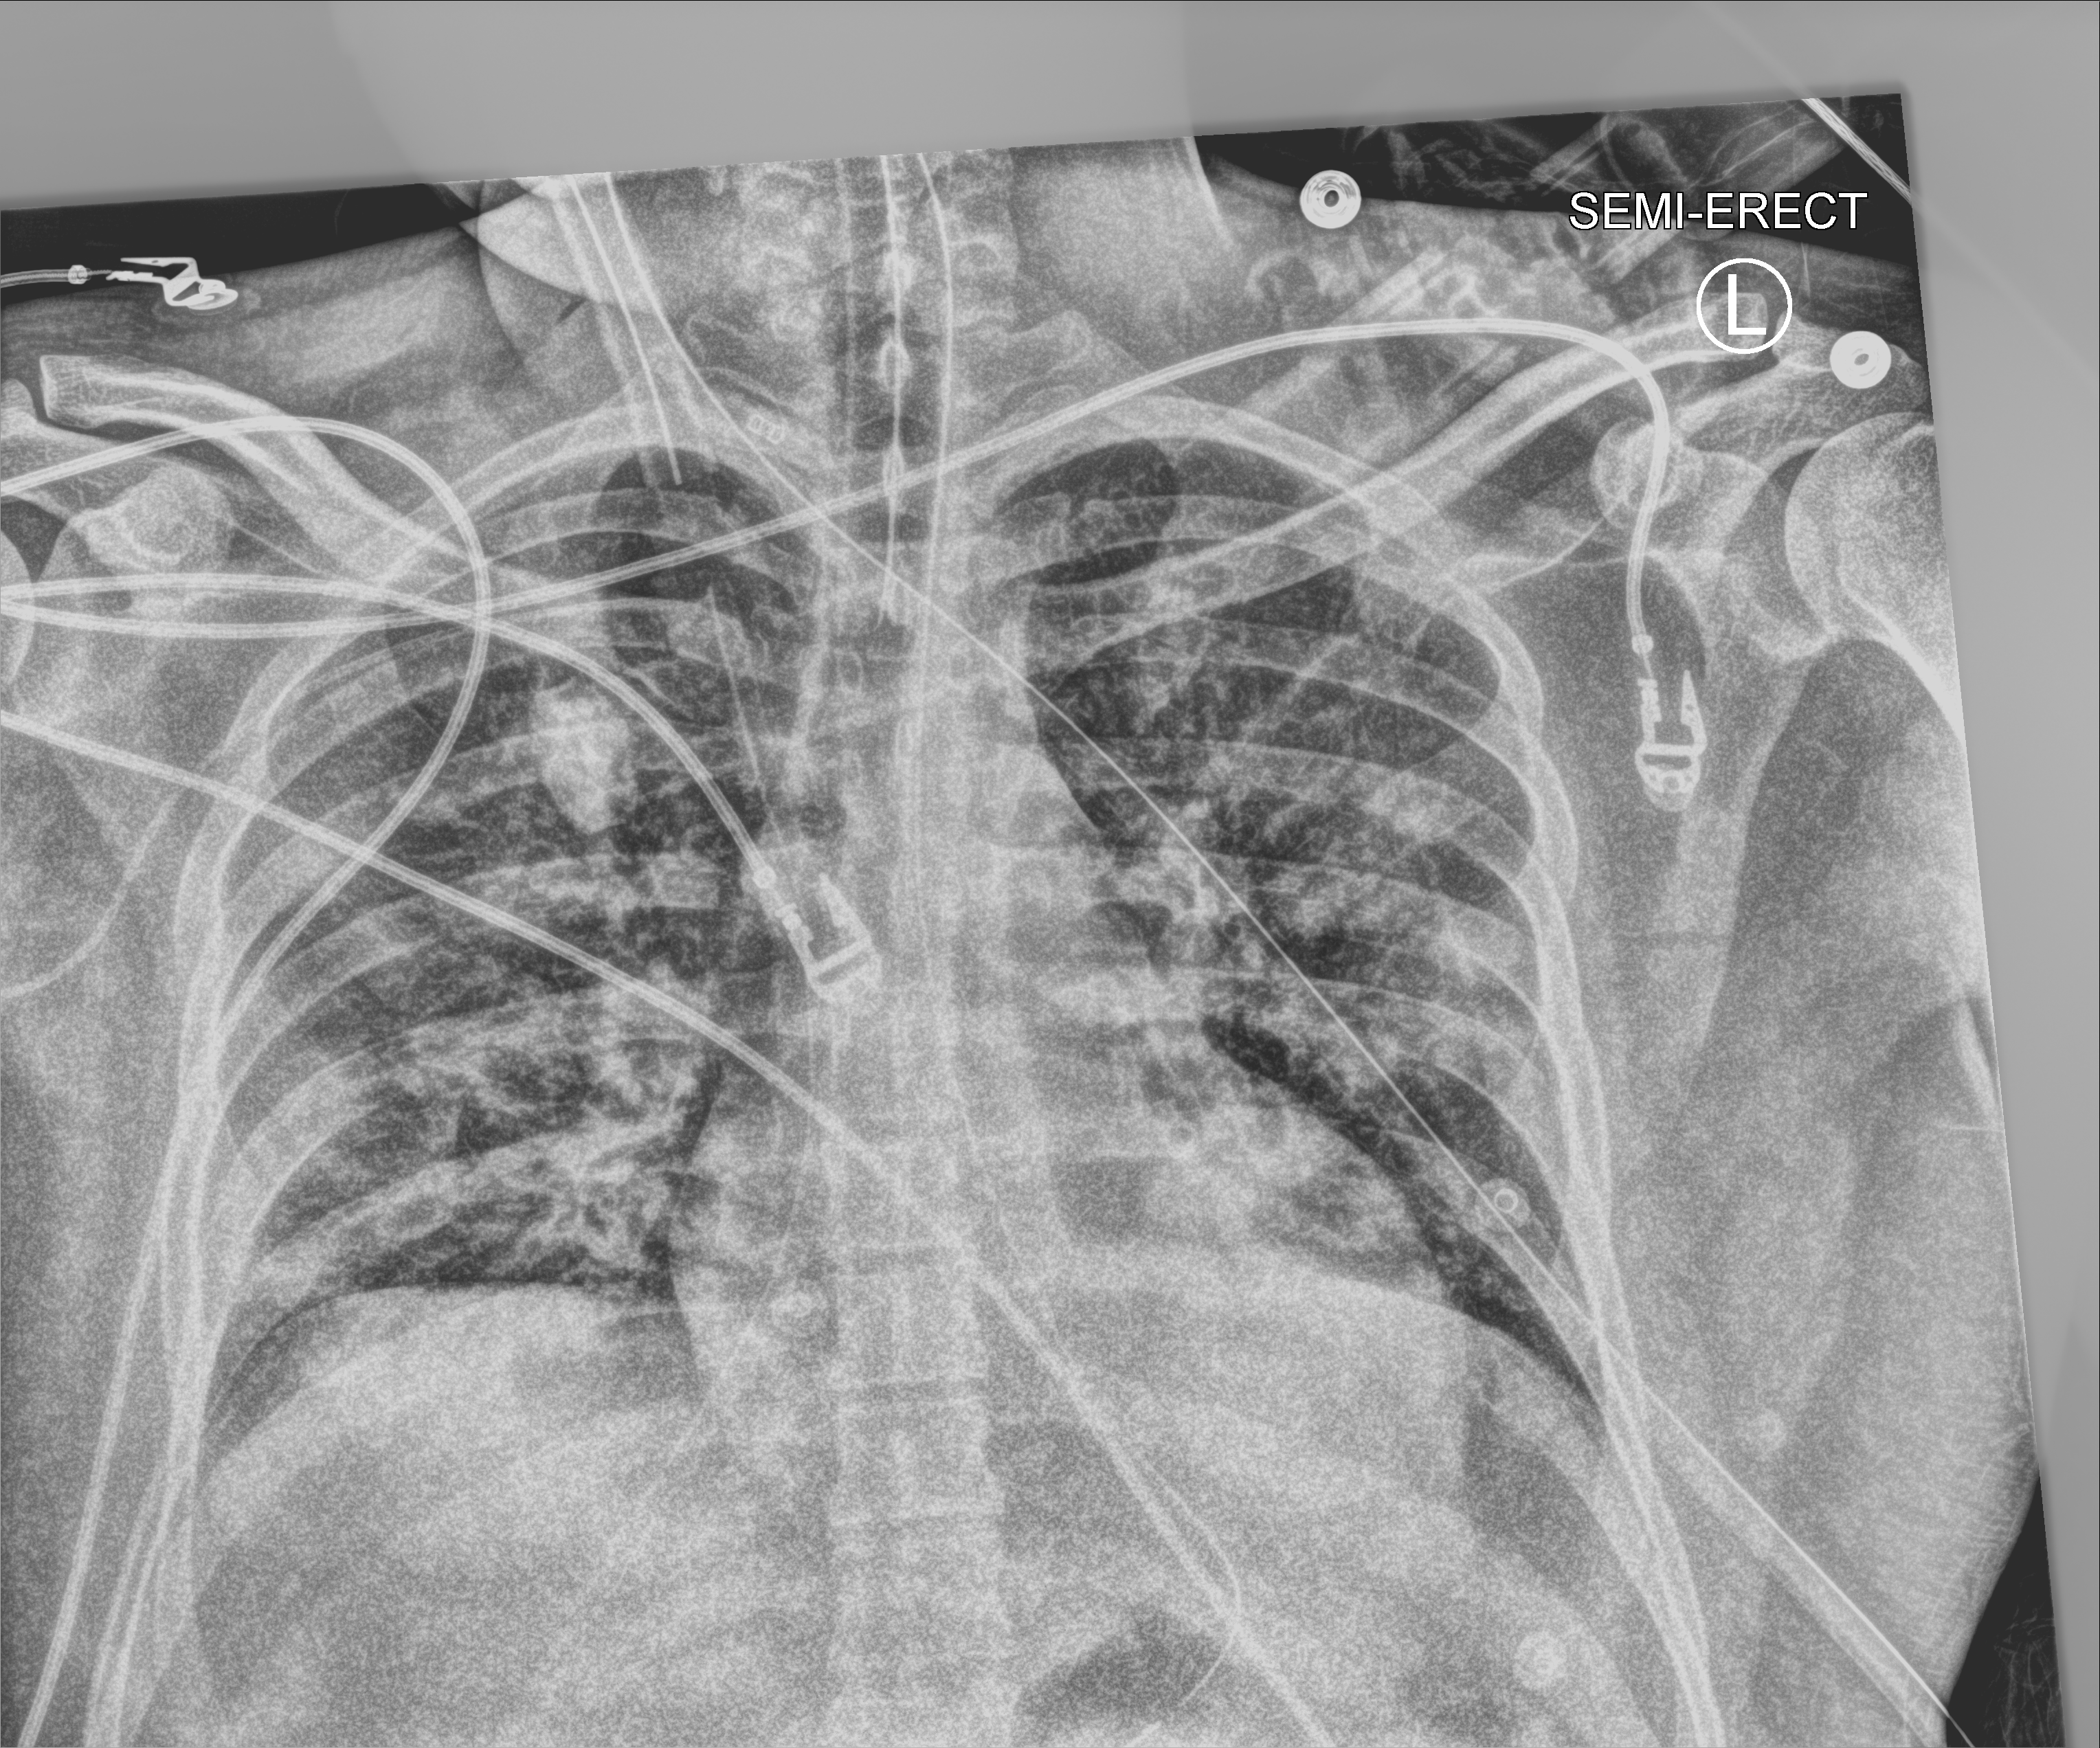
Chest X-ray (portable), anteroposterior (AP) projection. Male patient hospitalised with COVID-19, age 18–59 years.
Admission-level facts for this patient (not findings on this image; timing relative to this image not recorded): admitted to intensive care during this hospital stay: yes; mechanically ventilated during this hospital stay: yes.